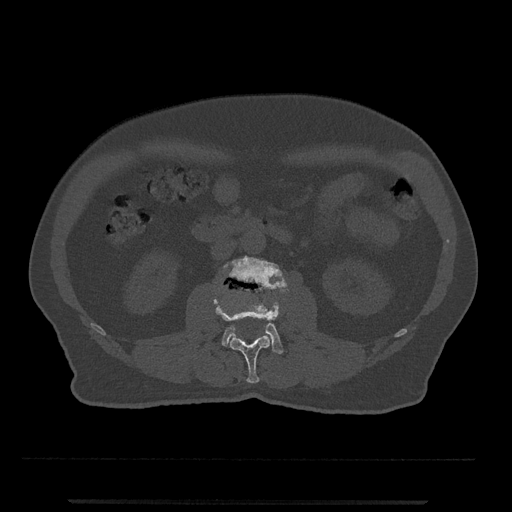
CT including the spine, one axial slice; reconstruction kernel Br40s/3; 120 kVp; bone window (W 1800 / L 400 HU); 0.5 mm slice thickness; 512 × 512 image matrix. Patient: male, 63 years. From the clinical record (not read from this slice): primary cancer: prostate.
Annotated regions visible in this slice (semi-automatic segmentation, software-assisted and operator-edited):
- L2 vertebra: bounding box (x1, y1, x2, y2) in pixels: (214, 287, 279, 383)
- L3 vertebra: (222, 256, 286, 354)